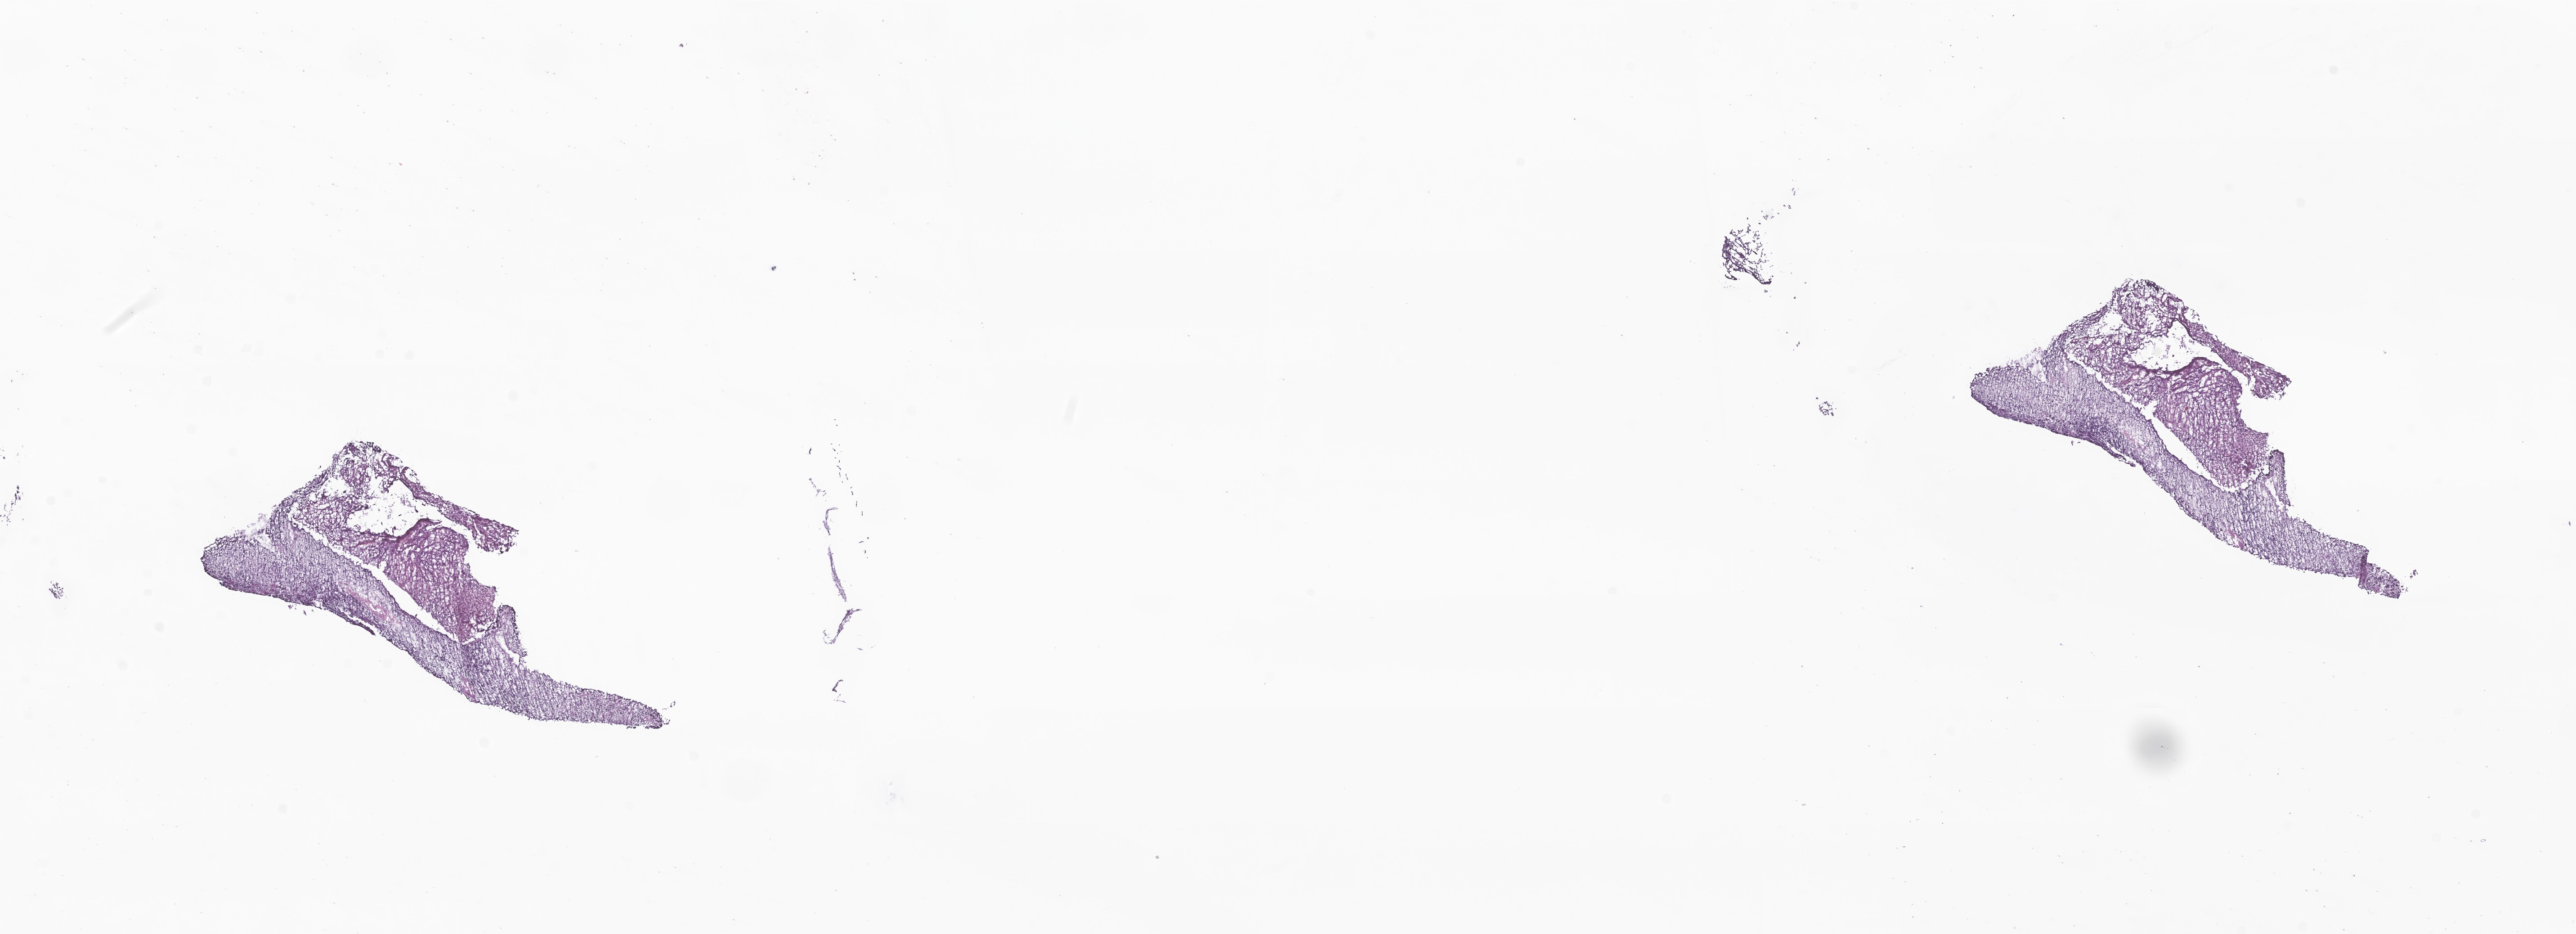
Haematoxylin and eosin whole-slide image of tumor tissue from the cerebellum — a low-resolution overview of the entire scanned area, about 24.1 x 8.8 mm, frozen section (OCT-embedded). Male patient, age 97 months.
Diagnosis (ICD-O-3 morphology term): Medulloblastoma, NOS.